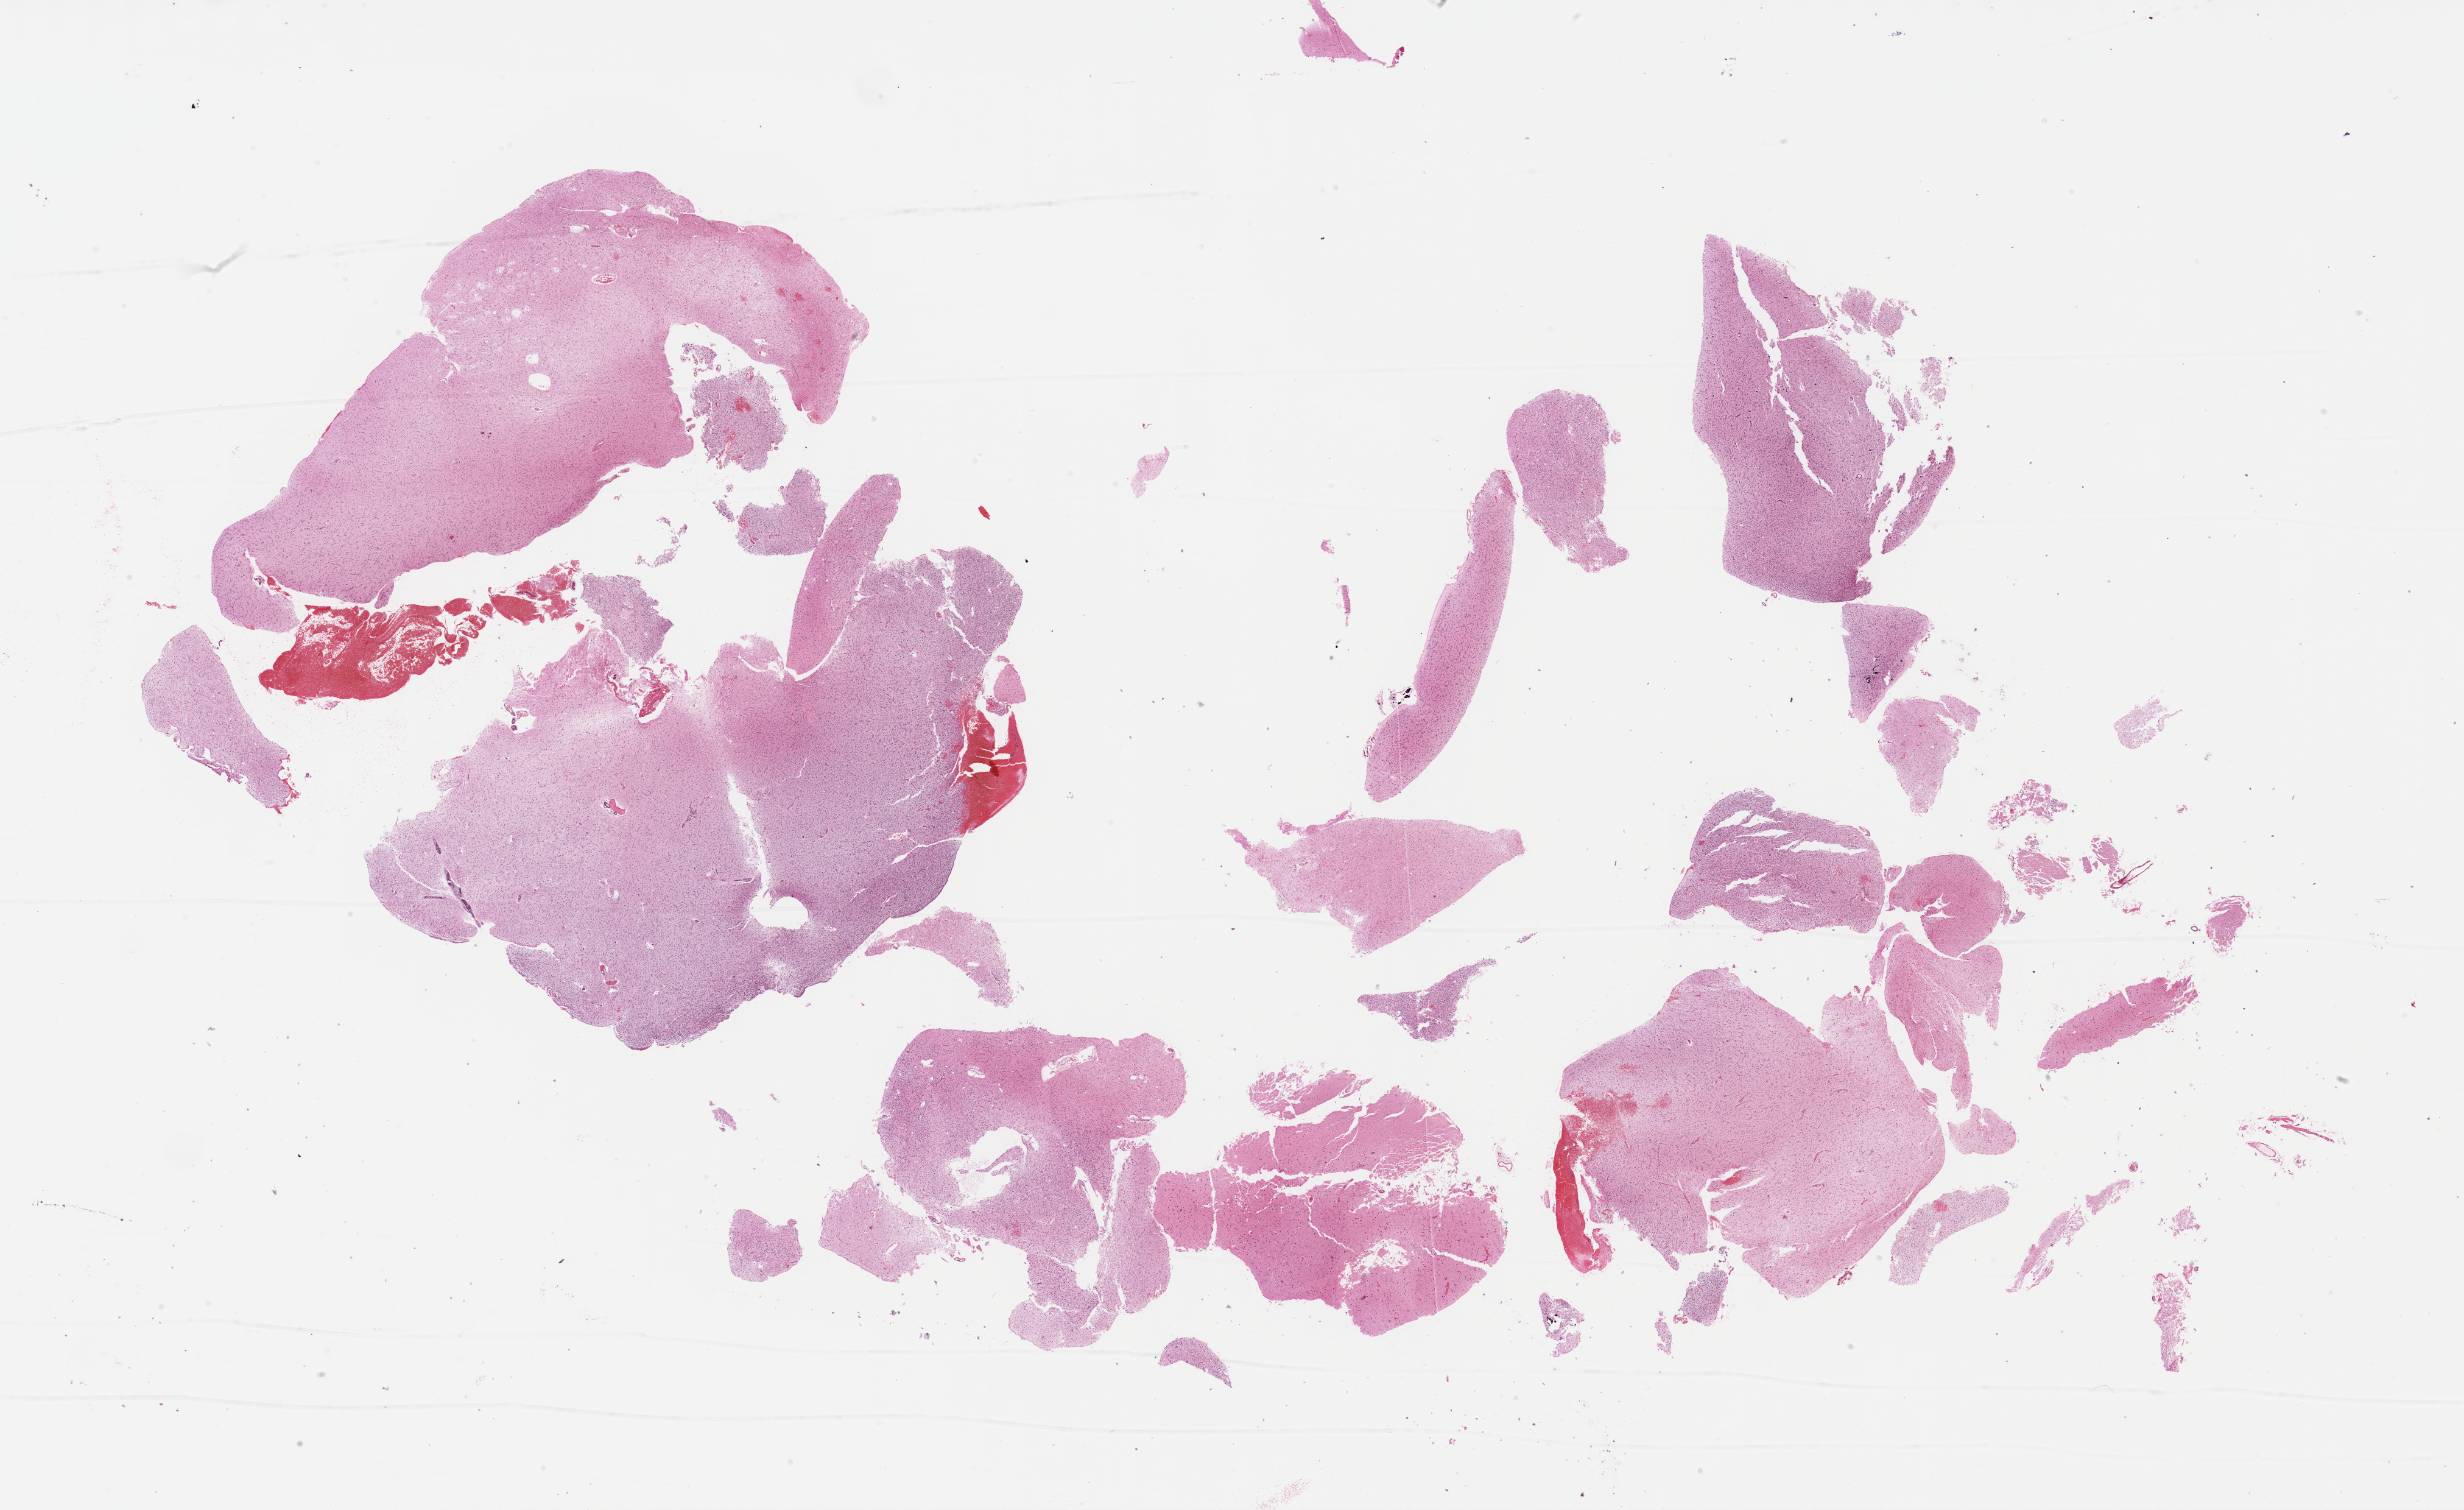
Digitized Hematoxylin and eosin (H&E) stained tissue section (whole slide) — a low-resolution overview of the entire scanned area, about 32.7 x 20.0 mm, formalin-fixed paraffin-embedded (FFPE) diagnostic section, sample: primary tumour, brain. Patient: male, age at initial diagnosis 36 years.
Diagnosis: Oligodendroglioma, anaplastic (cerebrum).